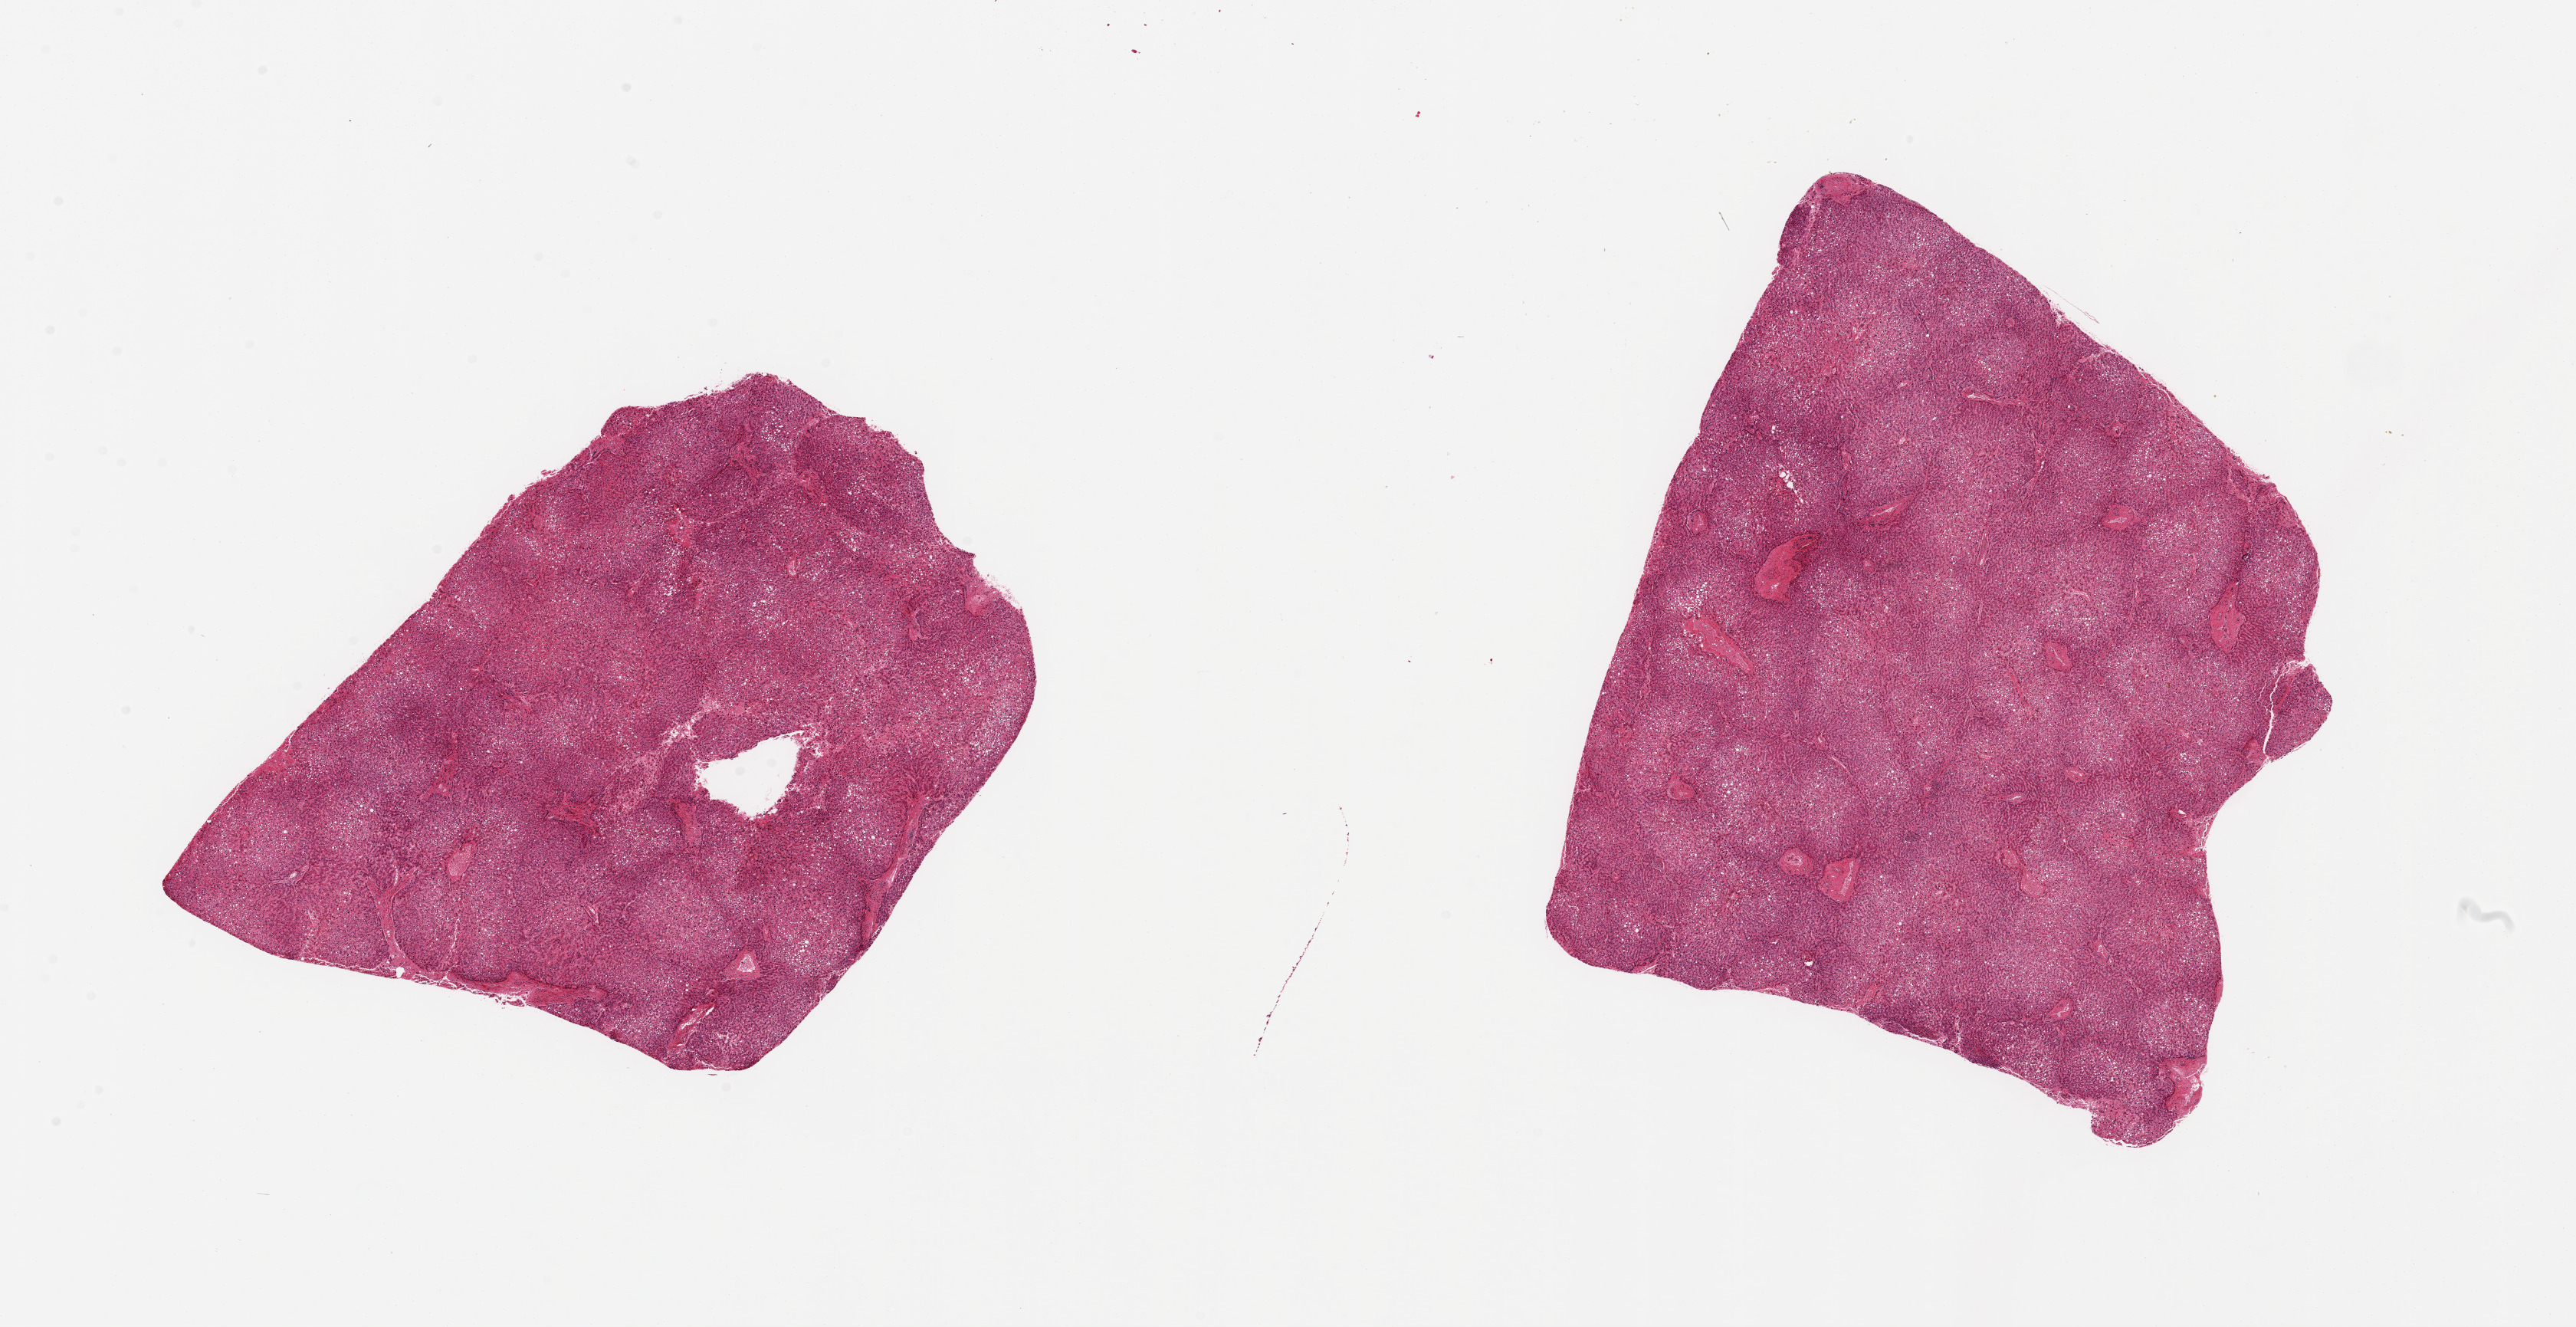
Whole-slide image, hematoxylin and eosin (H&E) stain — a low-resolution overview of the entire scanned area, about 26.6 x 13.7 mm, PAXgene-fixed, paraffin-embedded tissue, target tissue: liver, donor tissue sample. Donor: male.
• reviewer comment on this tissue sample: 2 pieces; marked central fatty degeneration, perivenular and periportal fibrosis